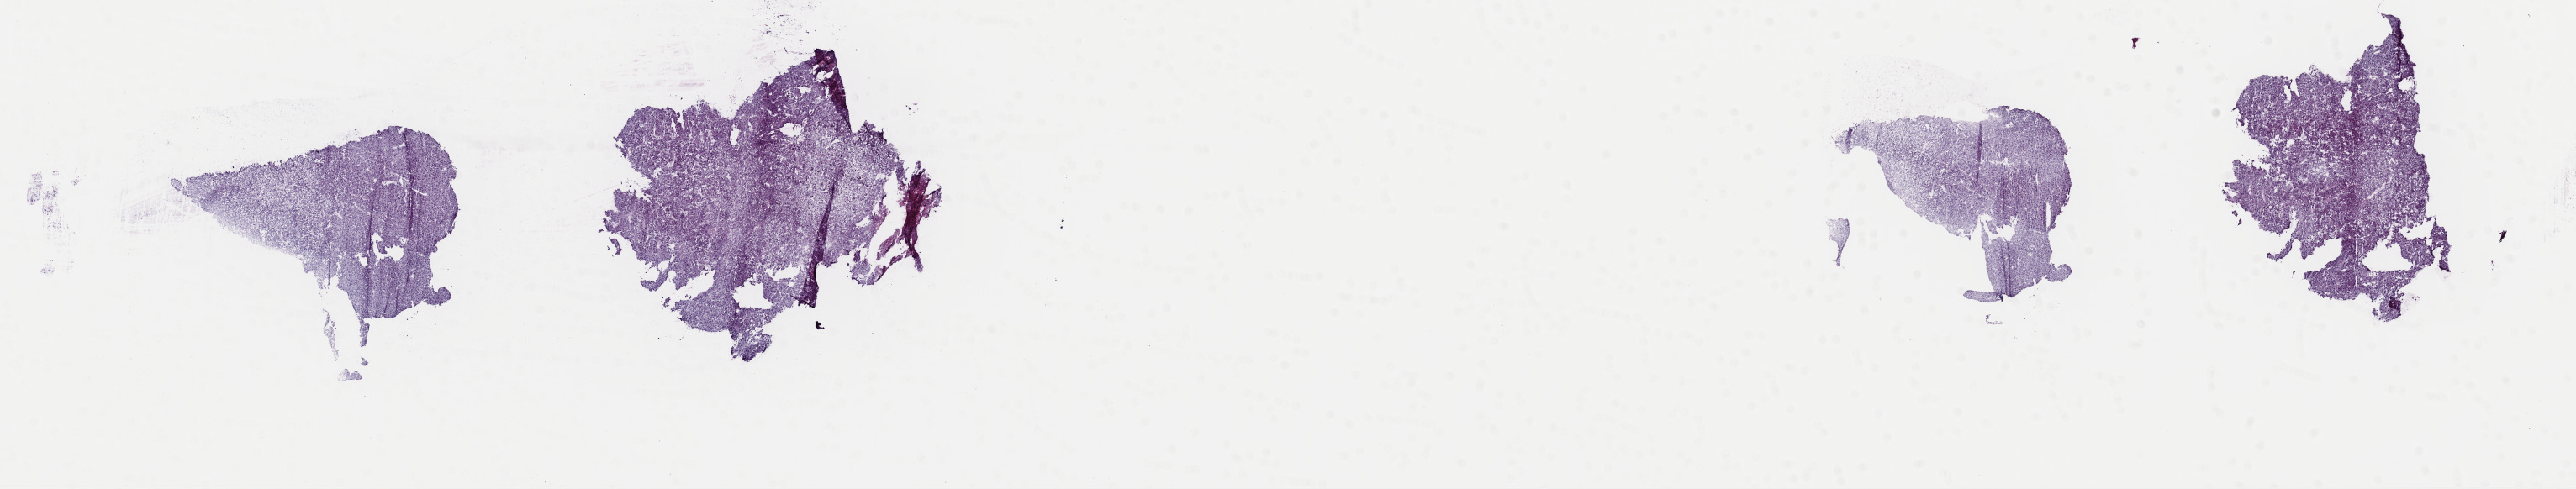
Whole-slide histology image, Hematoxylin and eosin (H&E) stained, shown as a low-resolution overview of the whole scanned area (about 24.2 x 4.6 mm, acquisition: 40x scan); frozen section from the top of the tissue portion; liver, primary tumour sample. Patient: male, age at initial diagnosis 63 years. Histologic grade: G3 (poorly differentiated). Slide review estimates, as recorded: tumour cells 100%, tumour nuclei 80%, normal cells 0%, stromal cells 0%, necrosis 0%. Infiltration values recorded for this section: lymphocyte infiltration 2%, monocyte infiltration 0%, neutrophil infiltration 0%.
• AJCC pathologic stage: I (7th edition)
• histologic diagnosis: Hepatocellular carcinoma, NOS